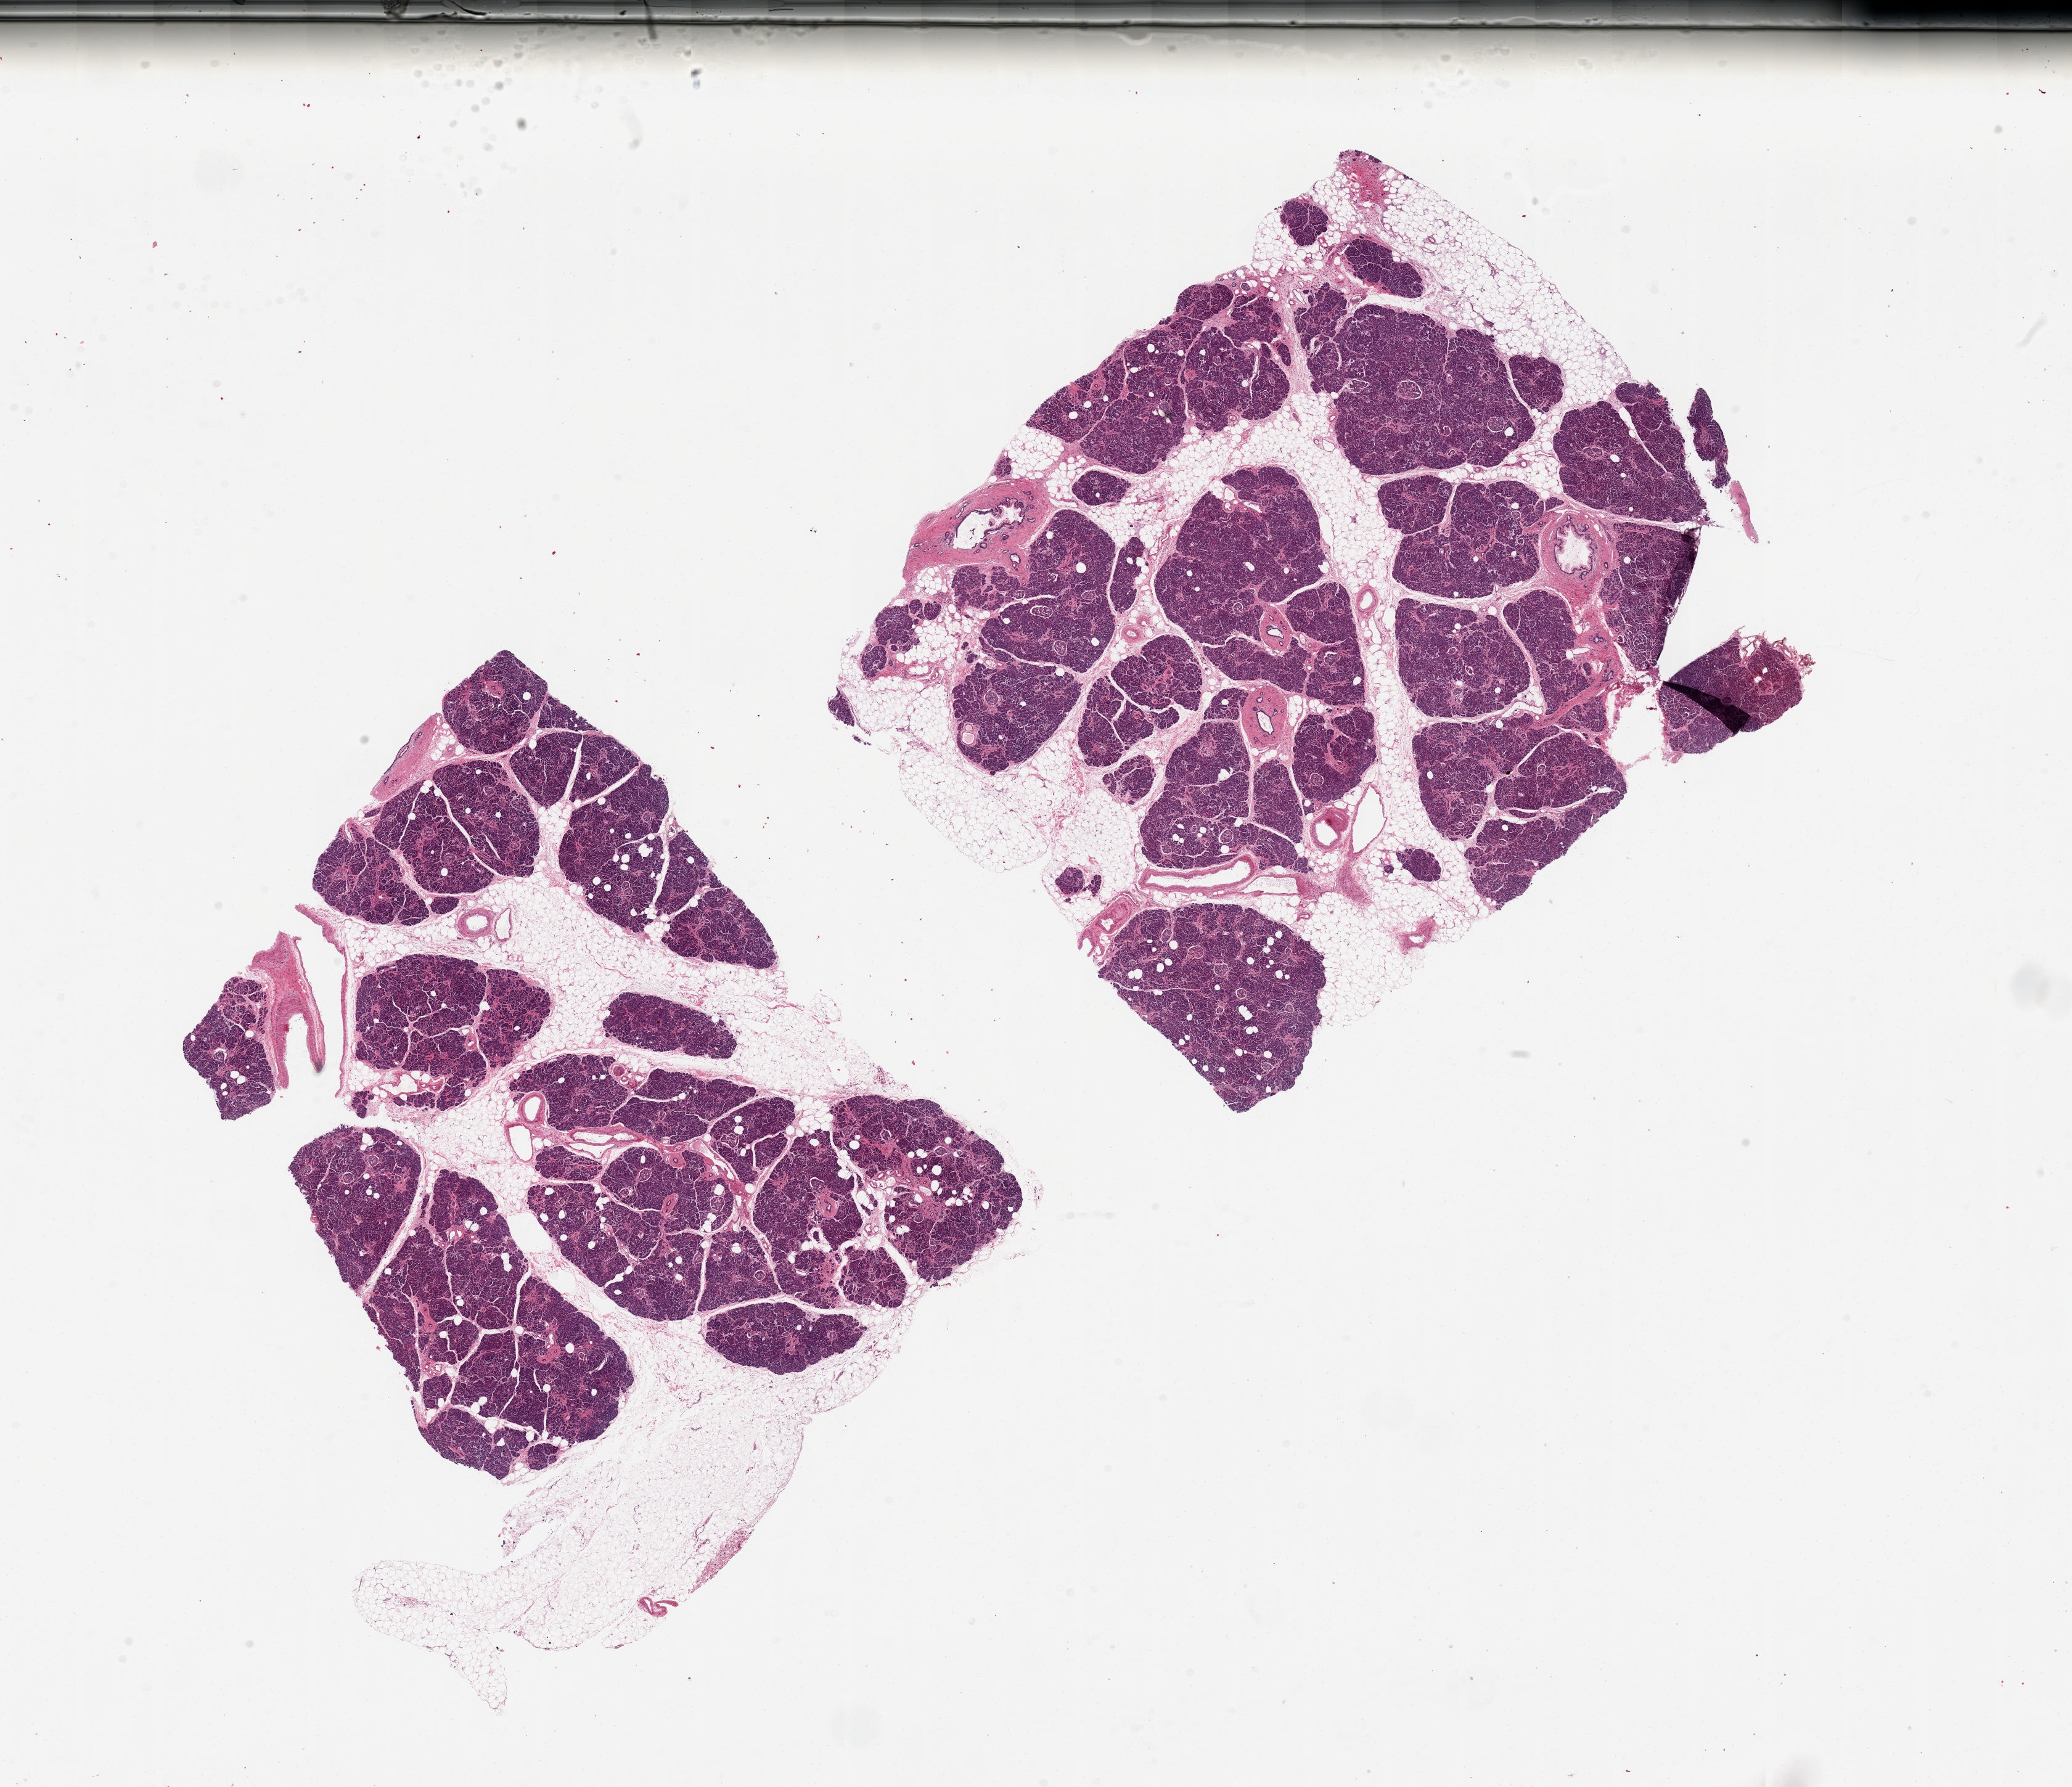
Digitized H&E-stained section, whole scanned area (about 26.6 x 22.9 mm, from a 20x scan) shown as a low-resolution overview. PAXgene-fixed, paraffin-embedded tissue. Target tissue: pancreas. Donor tissue sample.
Review note (as recorded): 2 pieces, 11x10 & 11x9mm. 30% internal and external adipose.